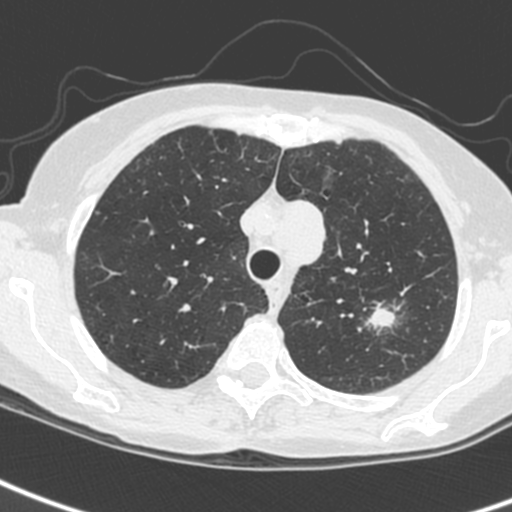
Low-dose screening chest CT, one axial slice; slice 196 of 242 in the series (ordered by position); 120 kVp; lung window (W 1500 / L -600 HU); 1.3 mm slice thickness; 512 × 512 image matrix.
Annotated regions visible in this slice (outlined manually by an expert reader):
- lesion 1 (tumor, upper lobe of left lung): bounding box <369,308,396,328> (left, top, right, bottom; pixels)
- lesion 3 (tumor, upper lobe of left lung): <293,200,326,265>